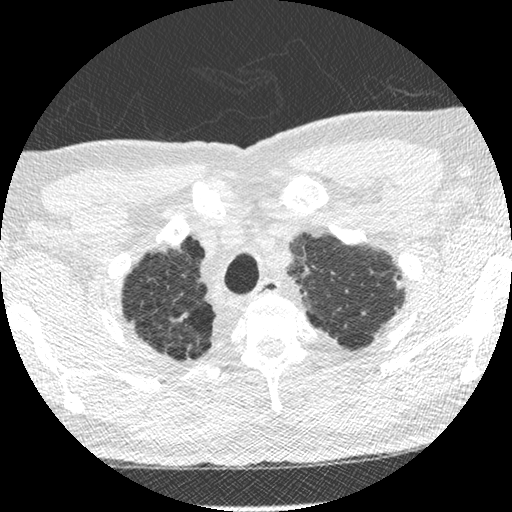
Low-dose screening chest CT, one axial slice; slice 248 of 275 in the series (ordered by position); reconstruction kernel STANDARD; lung window (W 1500 / L -600 HU); 1.25 mm slice thickness; 512 × 512 image matrix, field of view 330 × 330 mm.
Outlined on this slice (manually delineated by an expert):
- lesion 1 (tumor, upper lobe of left lung): bounding box (x1, y1, x2, y2) in pixels: (394, 273, 403, 289)